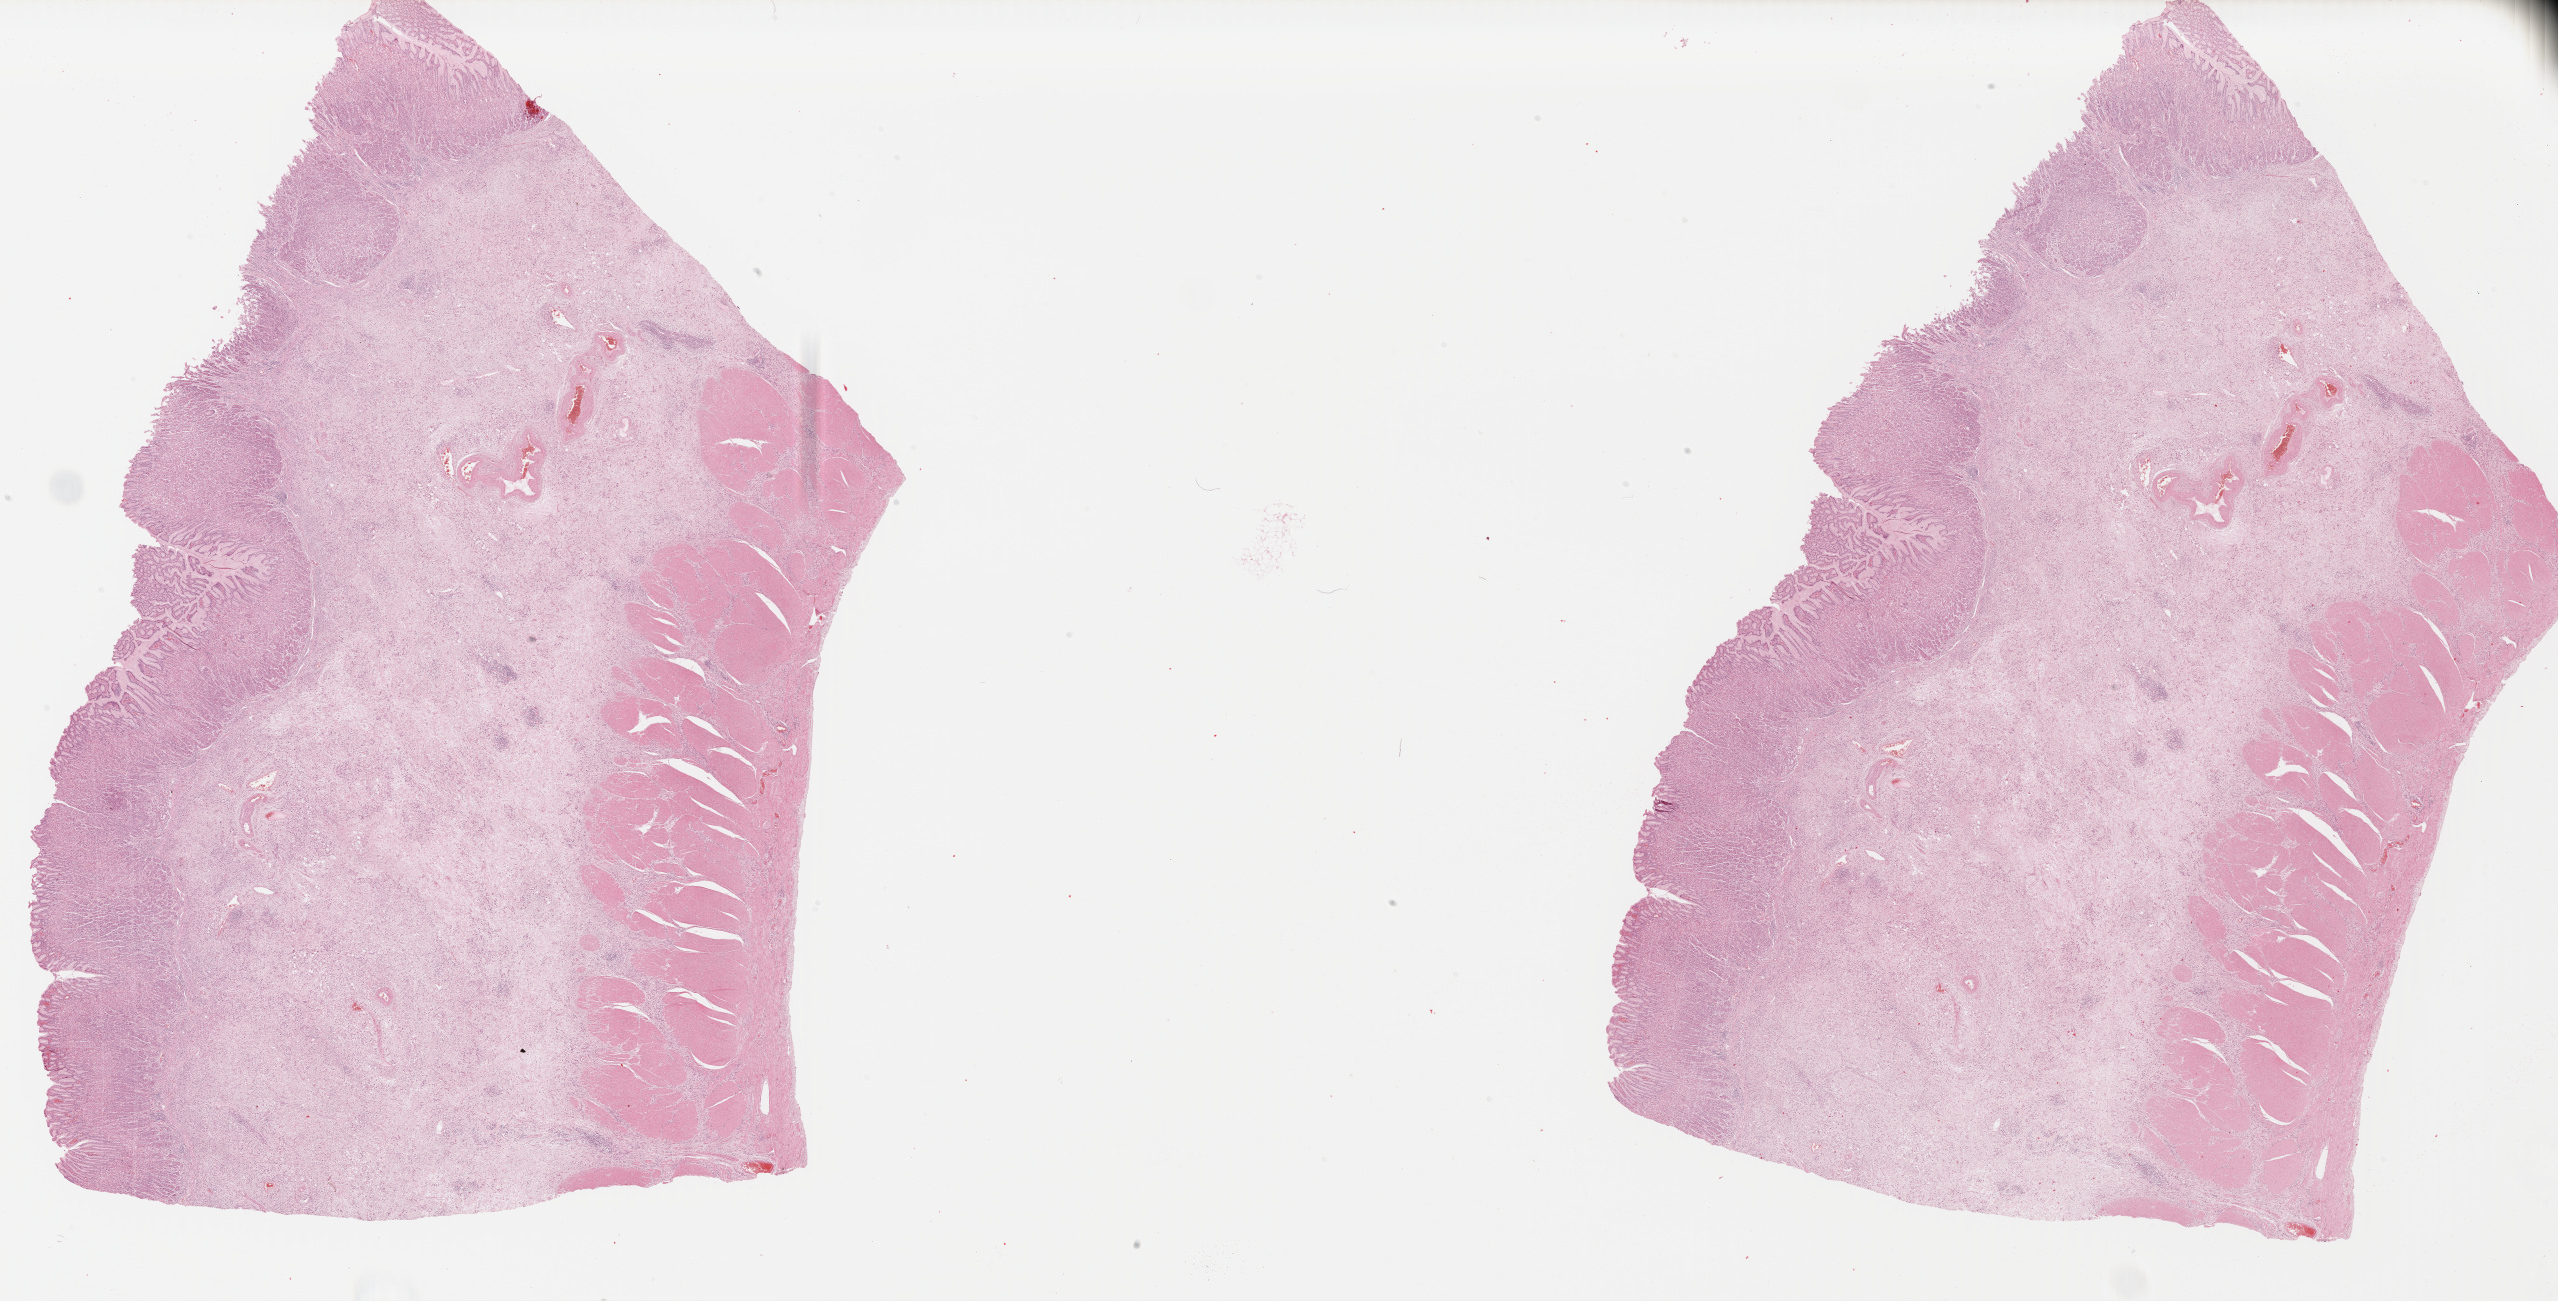
Digitized H&E tissue section (whole slide) — a low-resolution overview of the entire scanned area, about 40.2 x 20.5 mm (from a 40x scan); formalin-fixed paraffin-embedded (FFPE) diagnostic section; stomach, primary tumour sample. Male patient; age at initial diagnosis 75 years. Histologic grade: G3 (poorly differentiated).
AJCC pathologic stage: IIIA (7th edition). Pathologic diagnosis: Carcinoma, diffuse type (cardia, NOS).